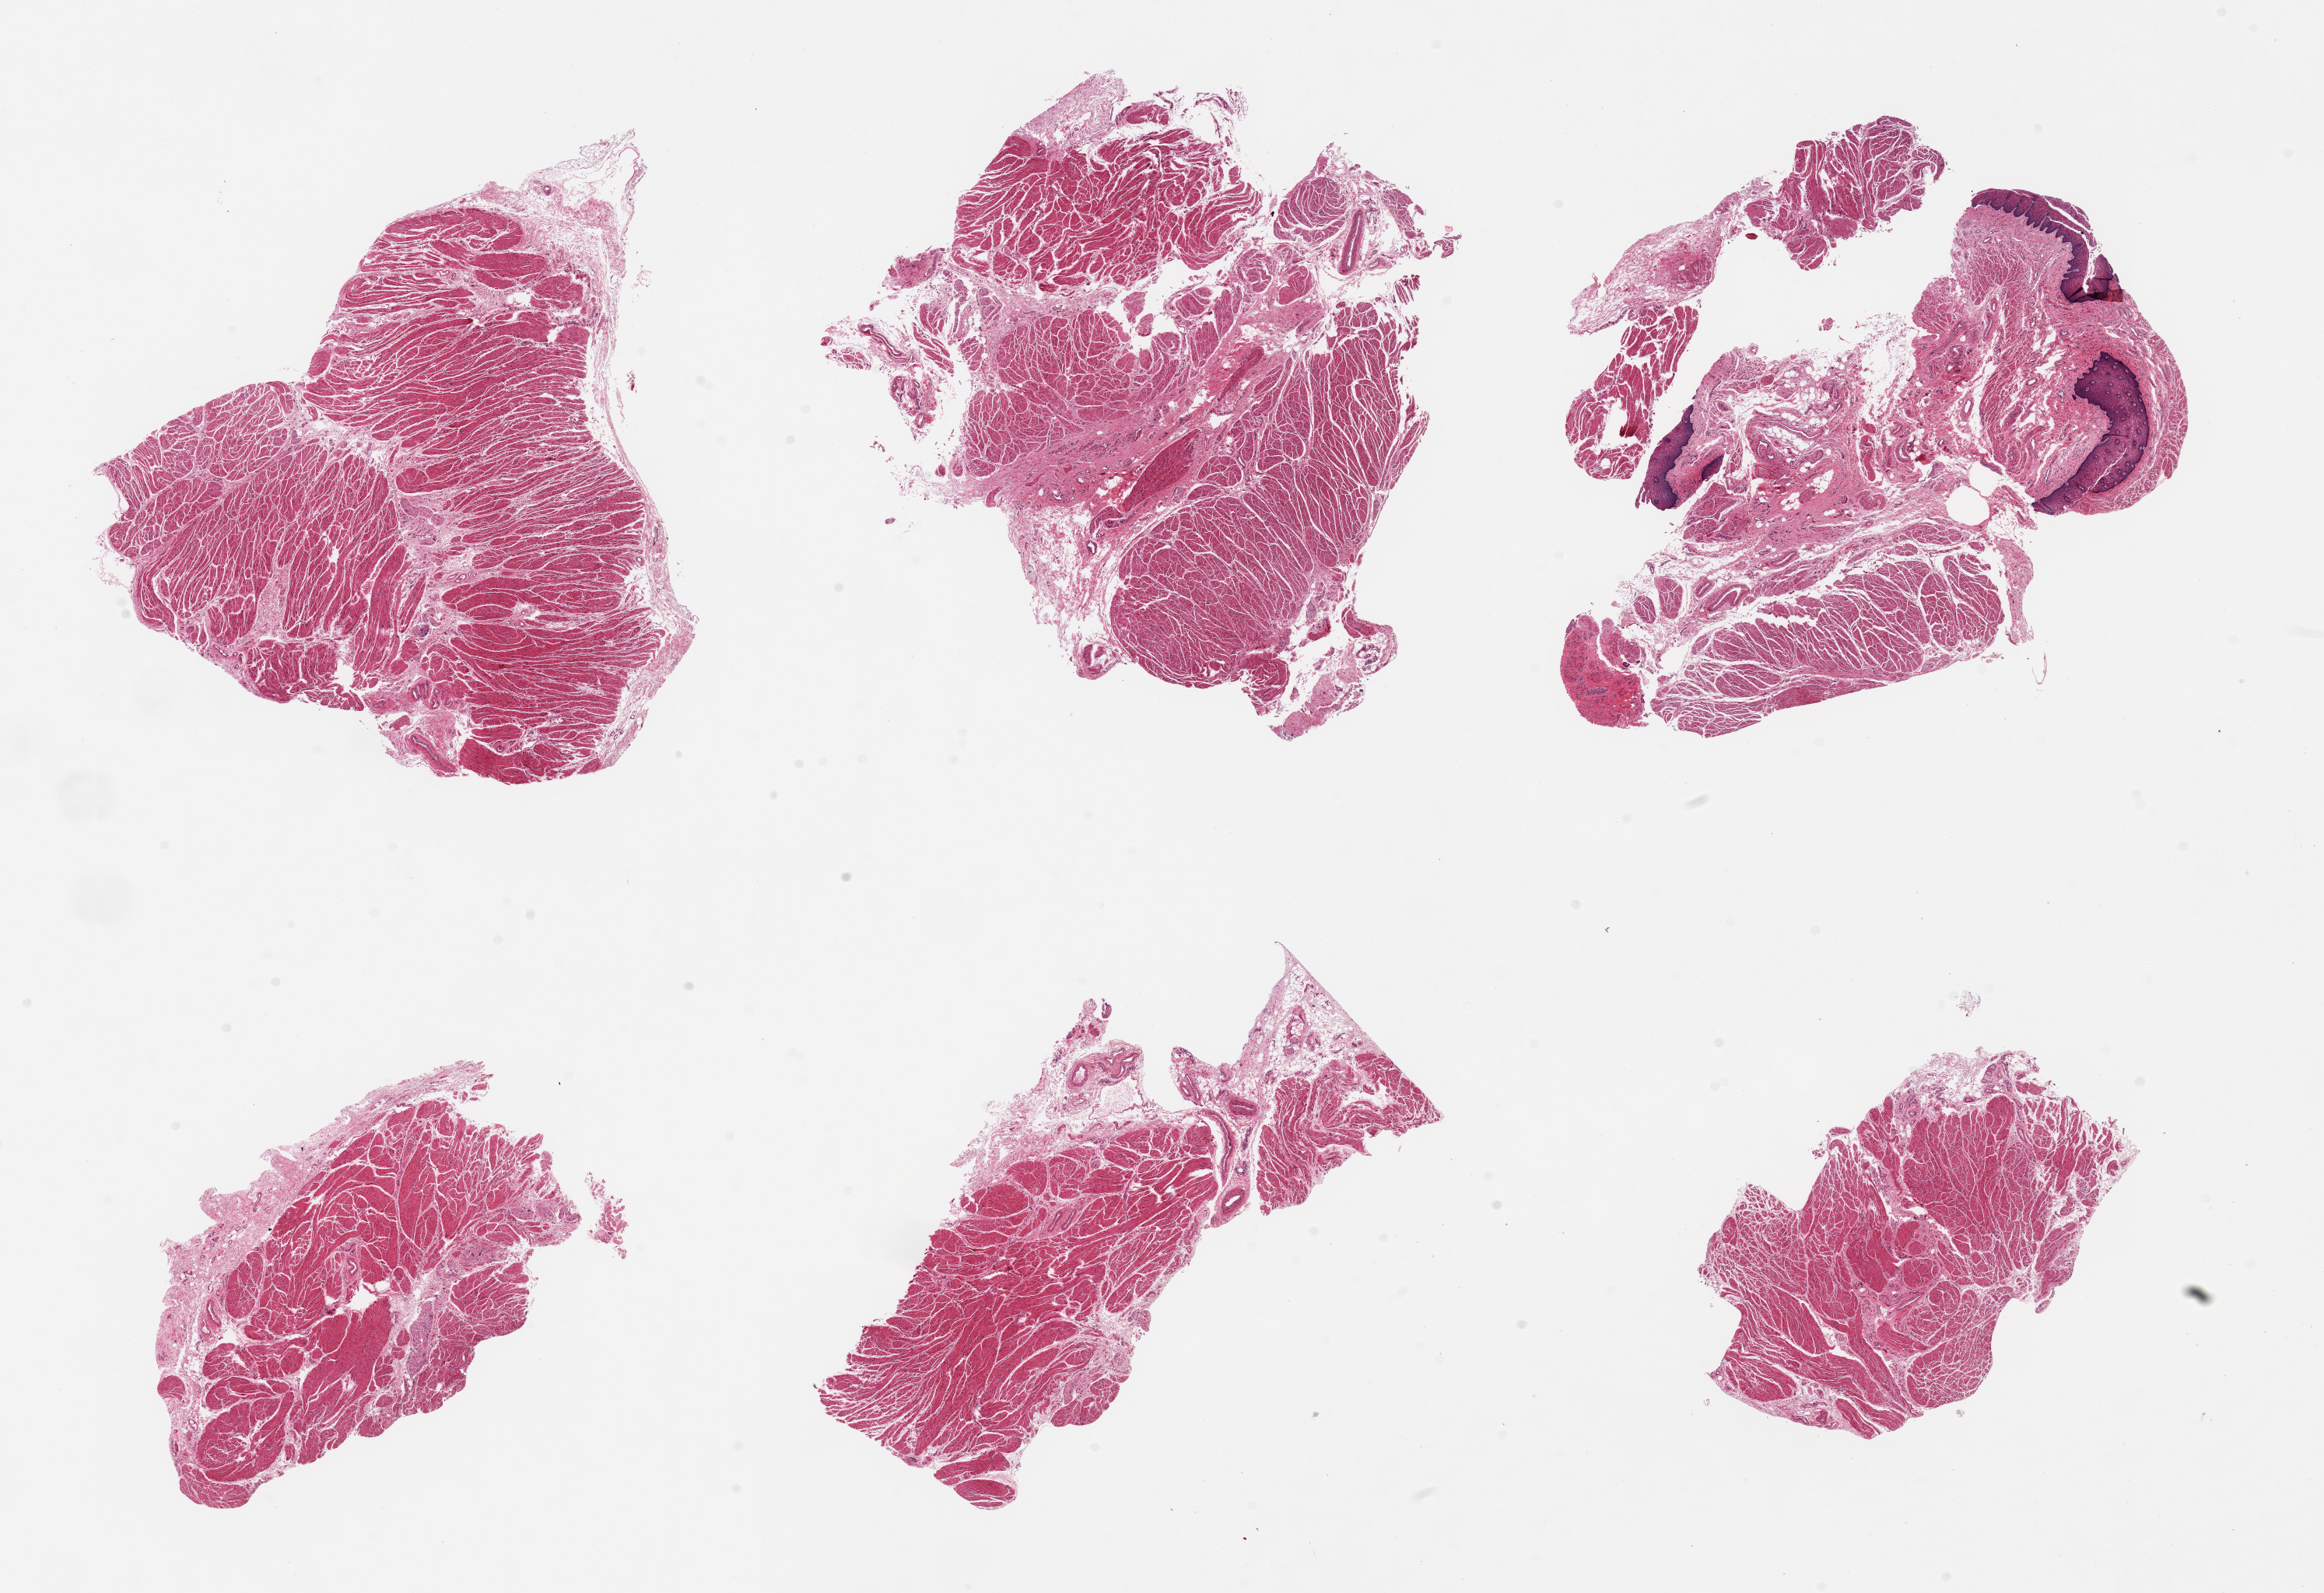
Whole-slide image, haematoxylin and eosin stain, brightfield, whole scanned area (about 23.6 x 16.2 mm) shown as a low-resolution overview, PAXgene-fixed, paraffin-embedded tissue, section of gastroesophageal junction (target tissue), tissue donor sample. Donor sex: female.
Pathologist's review note for this sample: 6 pieces, mainly target muscularis, few ~1mm foci of 'contaminant' squamous mucosa.